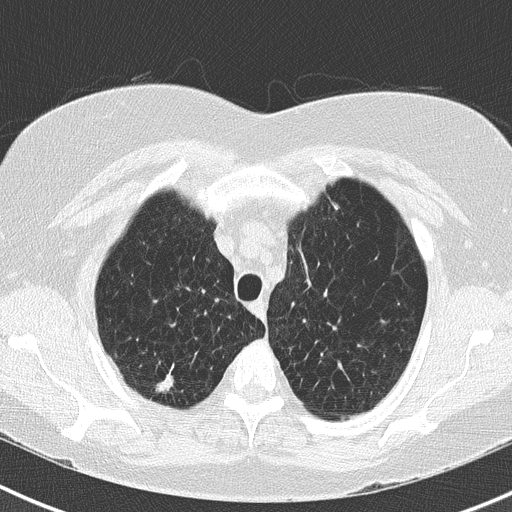
Chest CT (low-dose screening protocol), one axial image, second screening round (one year after baseline), lung window (W 1500 / L -600 HU), lung (sharp) reconstruction kernel (B50f). Female participant, aged 73 years at enrolment. Former smoker at enrolment.
Expert-annotated lung lesion, bounding box [x1, y1, x2, y2] px = [140, 362, 190, 403]. The screening reader recorded 2 non-calcified nodules or masses ≥4 mm on this exam; which of them this box marks is not recorded. Official screen result: positive, no significant change: stable abnormalities potentially related to lung cancer, unchanged since the prior screening exam.